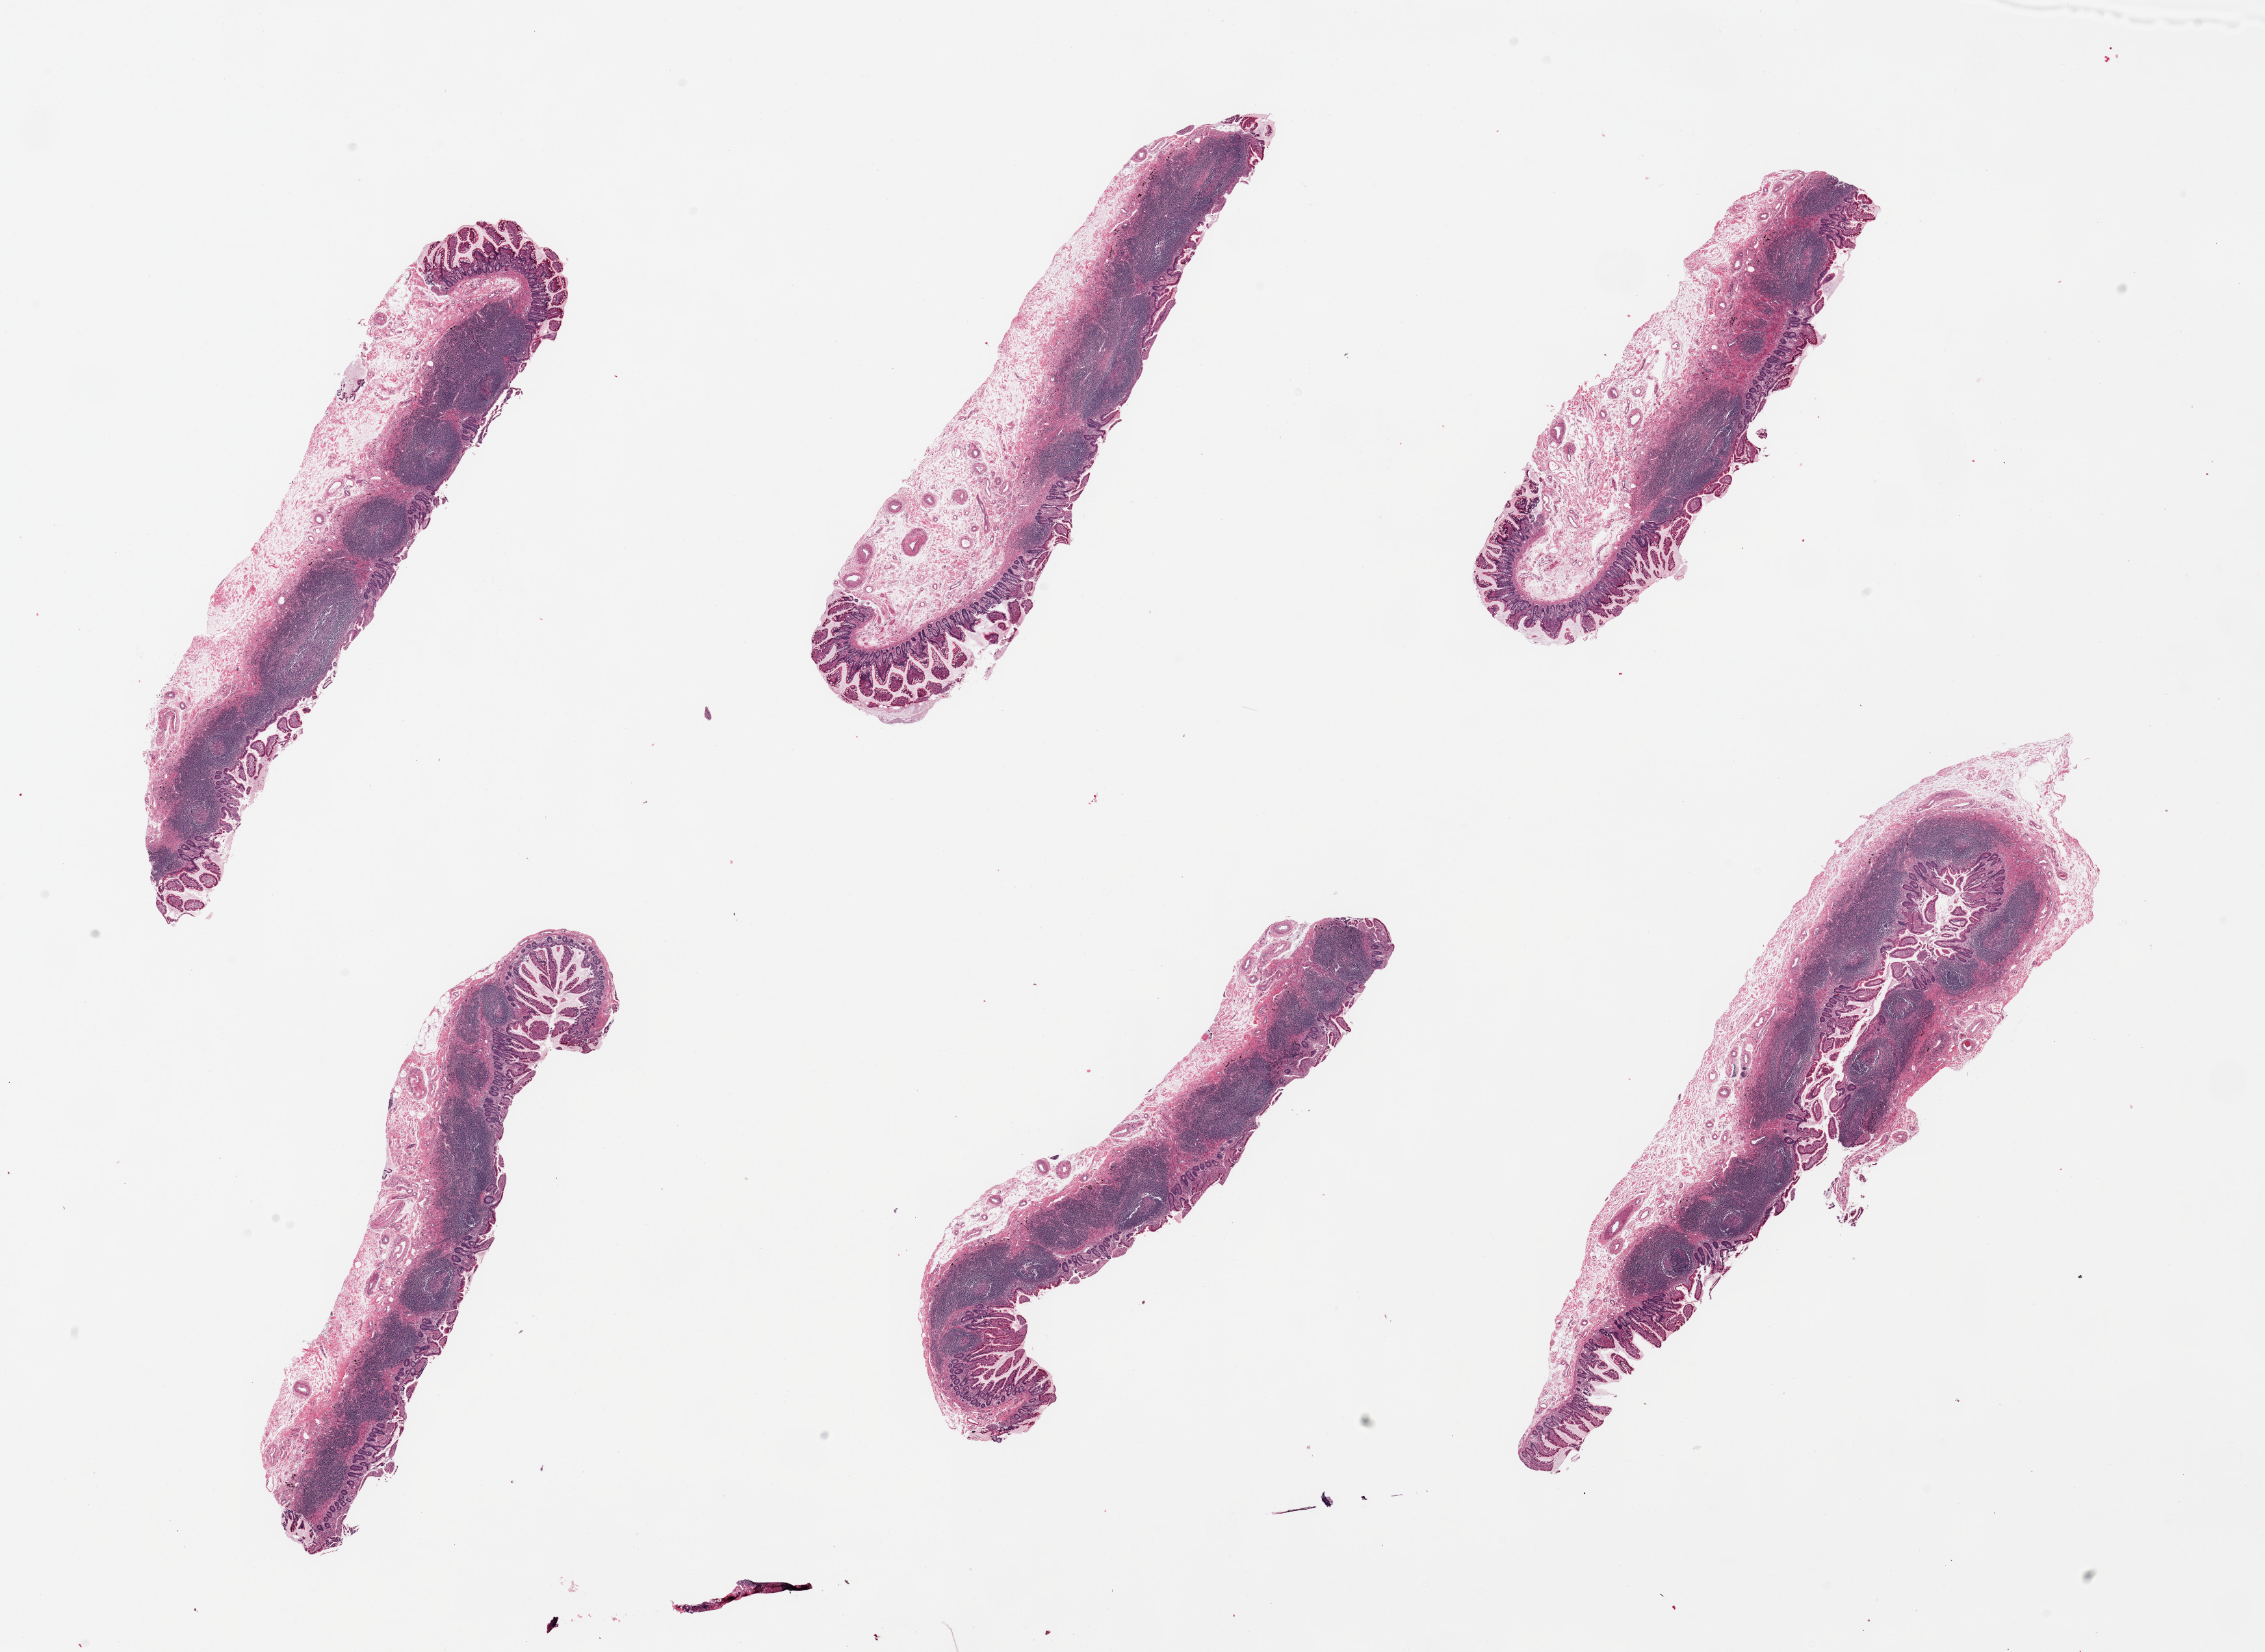
Hematoxylin and eosin (H&E) whole-slide image — a low-resolution overview of the entire scanned area, about 27.6 x 20.1 mm. PAXgene-fixed paraffin-embedded (PFPE) section. Sampled site (target tissue): ileum. Donor tissue sample. Female donor.
Reviewer comment on this tissue sample: 6 pieces, well-preserved, ~40% target lymphoid aggregates.